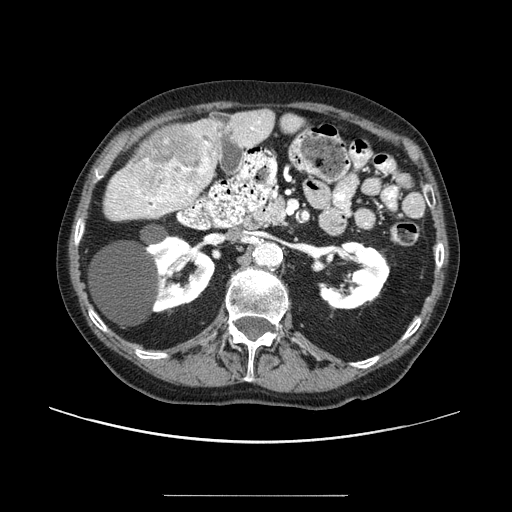
Contrast-enhanced abdominal CT (liver protocol), one axial slice. Position 38 of 91 along the scan axis. Reconstruction kernel STANDARD. One of 2 acquisitions stored at this slice position. Soft-tissue window (W 400 / L 40 HU). 2.5 mm slice thickness. 512 × 512 image matrix, field of view 400 × 400 mm. Case-level facts recorded for this patient, not image findings: diagnosis: hepatocellular carcinoma (patient treated with transarterial chemoembolisation; whether this scan precedes or follows treatment is not stated here); TNM stage (as recorded): Stage-I; Child-Pugh class: A; tumour differentiation: moderately differentiated.
Outlined on this slice (semi-automatic segmentation, software-assisted and operator-edited):
- liver parenchyma outside the tumour (the mass and vessels are separate outlines, so this box may not span the whole liver): bounding box (x1, y1, x2, y2) in pixels: (106, 110, 274, 220)
- mass: (130, 123, 214, 205)
- liver vessels: (114, 120, 261, 214)